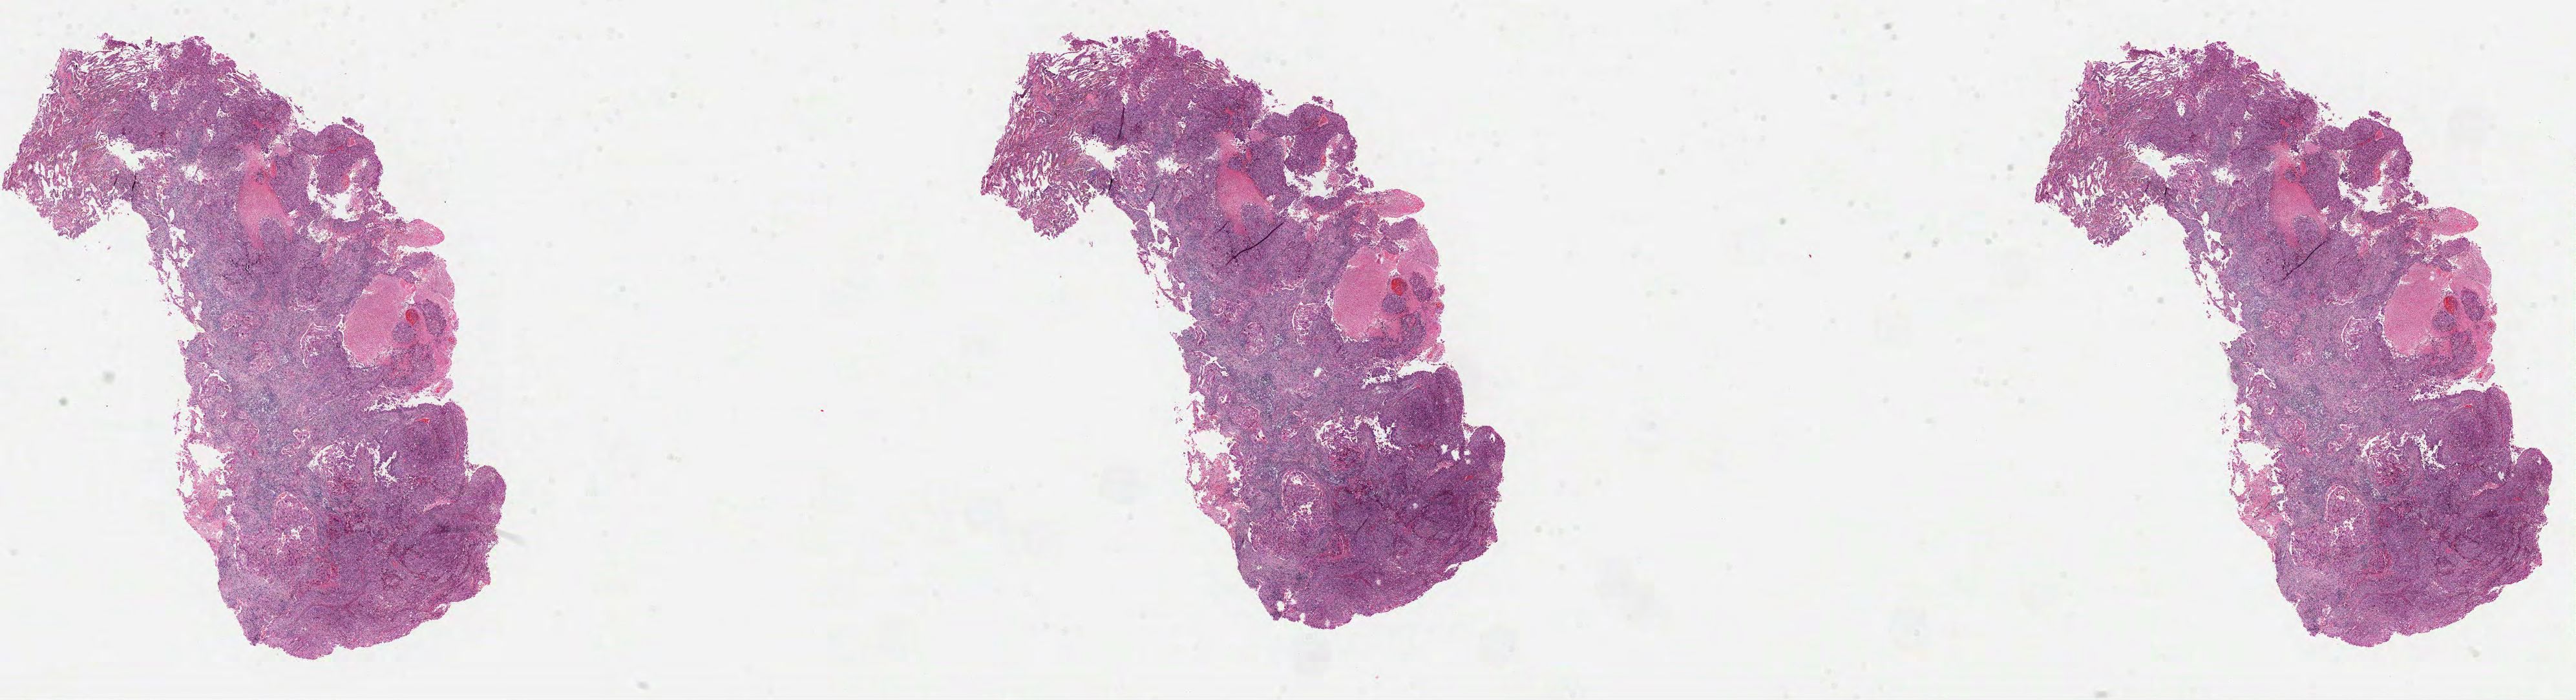
Whole-slide histology image, H&E — a low-resolution overview of the entire scanned area, about 32.1 x 8.7 mm (from a 40x scan), formalin-fixed paraffin-embedded (FFPE) diagnostic section, lung, primary tumour sample. Male patient; age at initial diagnosis 42 years.
Laterality: left. Histologic diagnosis: Adenocarcinoma, NOS. AJCC pathologic stage: IV (5th edition).